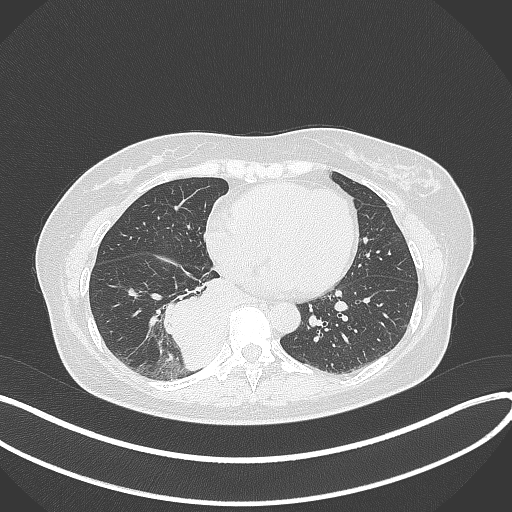
Chest CT, one axial slice; 120 kVp; lung window (W 1500 / L -600 HU); 1 mm slice thickness; 512 × 512 image matrix, field of view 400 × 400 mm. Patient: female, 54 years. From the clinical record (not read from this slice): clinical TNM (as recorded): T4 N0 M0.
Outlined on this slice (bounding box drawn by a radiologist):
- lung tumour (recorded histology: adenocarcinoma): bounding box (x1, y1, x2, y2) in pixels: (160, 275, 237, 375)